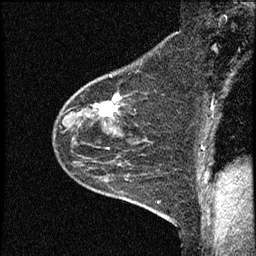
Breast MRI (dynamic contrast-enhanced), one sagittal slice. Slice 46 of 60 in the series (ordered by position). Dynamic contrast-enhanced study with each time point stored as its own series, time point 2 of 4 at this slice position (early post-contrast, ordered by acquisition time). 1.5 T. TE 4.2 ms, TR 17.6 ms. 2 mm slice thickness. 256 × 256 image matrix, field of view 200 × 200 mm. Female patient, age 53 years. Case-level facts recorded for this patient, not image findings: setting: breast cancer imaged before/during neoadjuvant chemotherapy; receptor status: HR-positive, HER2-negative.
Annotated regions visible in this slice (semi-automatically segmented with operator editing):
- analysis volume of interest (the breast-tissue region the enhancement analysis was run in; not a lesion): bounding box (x1, y1, x2, y2) in pixels: (53, 69, 153, 199)
- tumour enhancement mask (voxels above the 100 % enhancement threshold inside the analysis volume of interest): (78, 94, 120, 117)